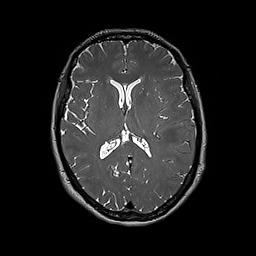
Brain MRI from a brain-tumour surgery series, one axial slice; 256 × 256 image matrix, field of view 250 × 250 mm. Case-level facts recorded for this patient, not image findings: histopathology: Glioblastoma; WHO grade: 4; IDH mutation: no.
Outlined on this slice (manually delineated by an expert):
- tumour: bounding box <181,131,193,169> (left, top, right, bottom; pixels)